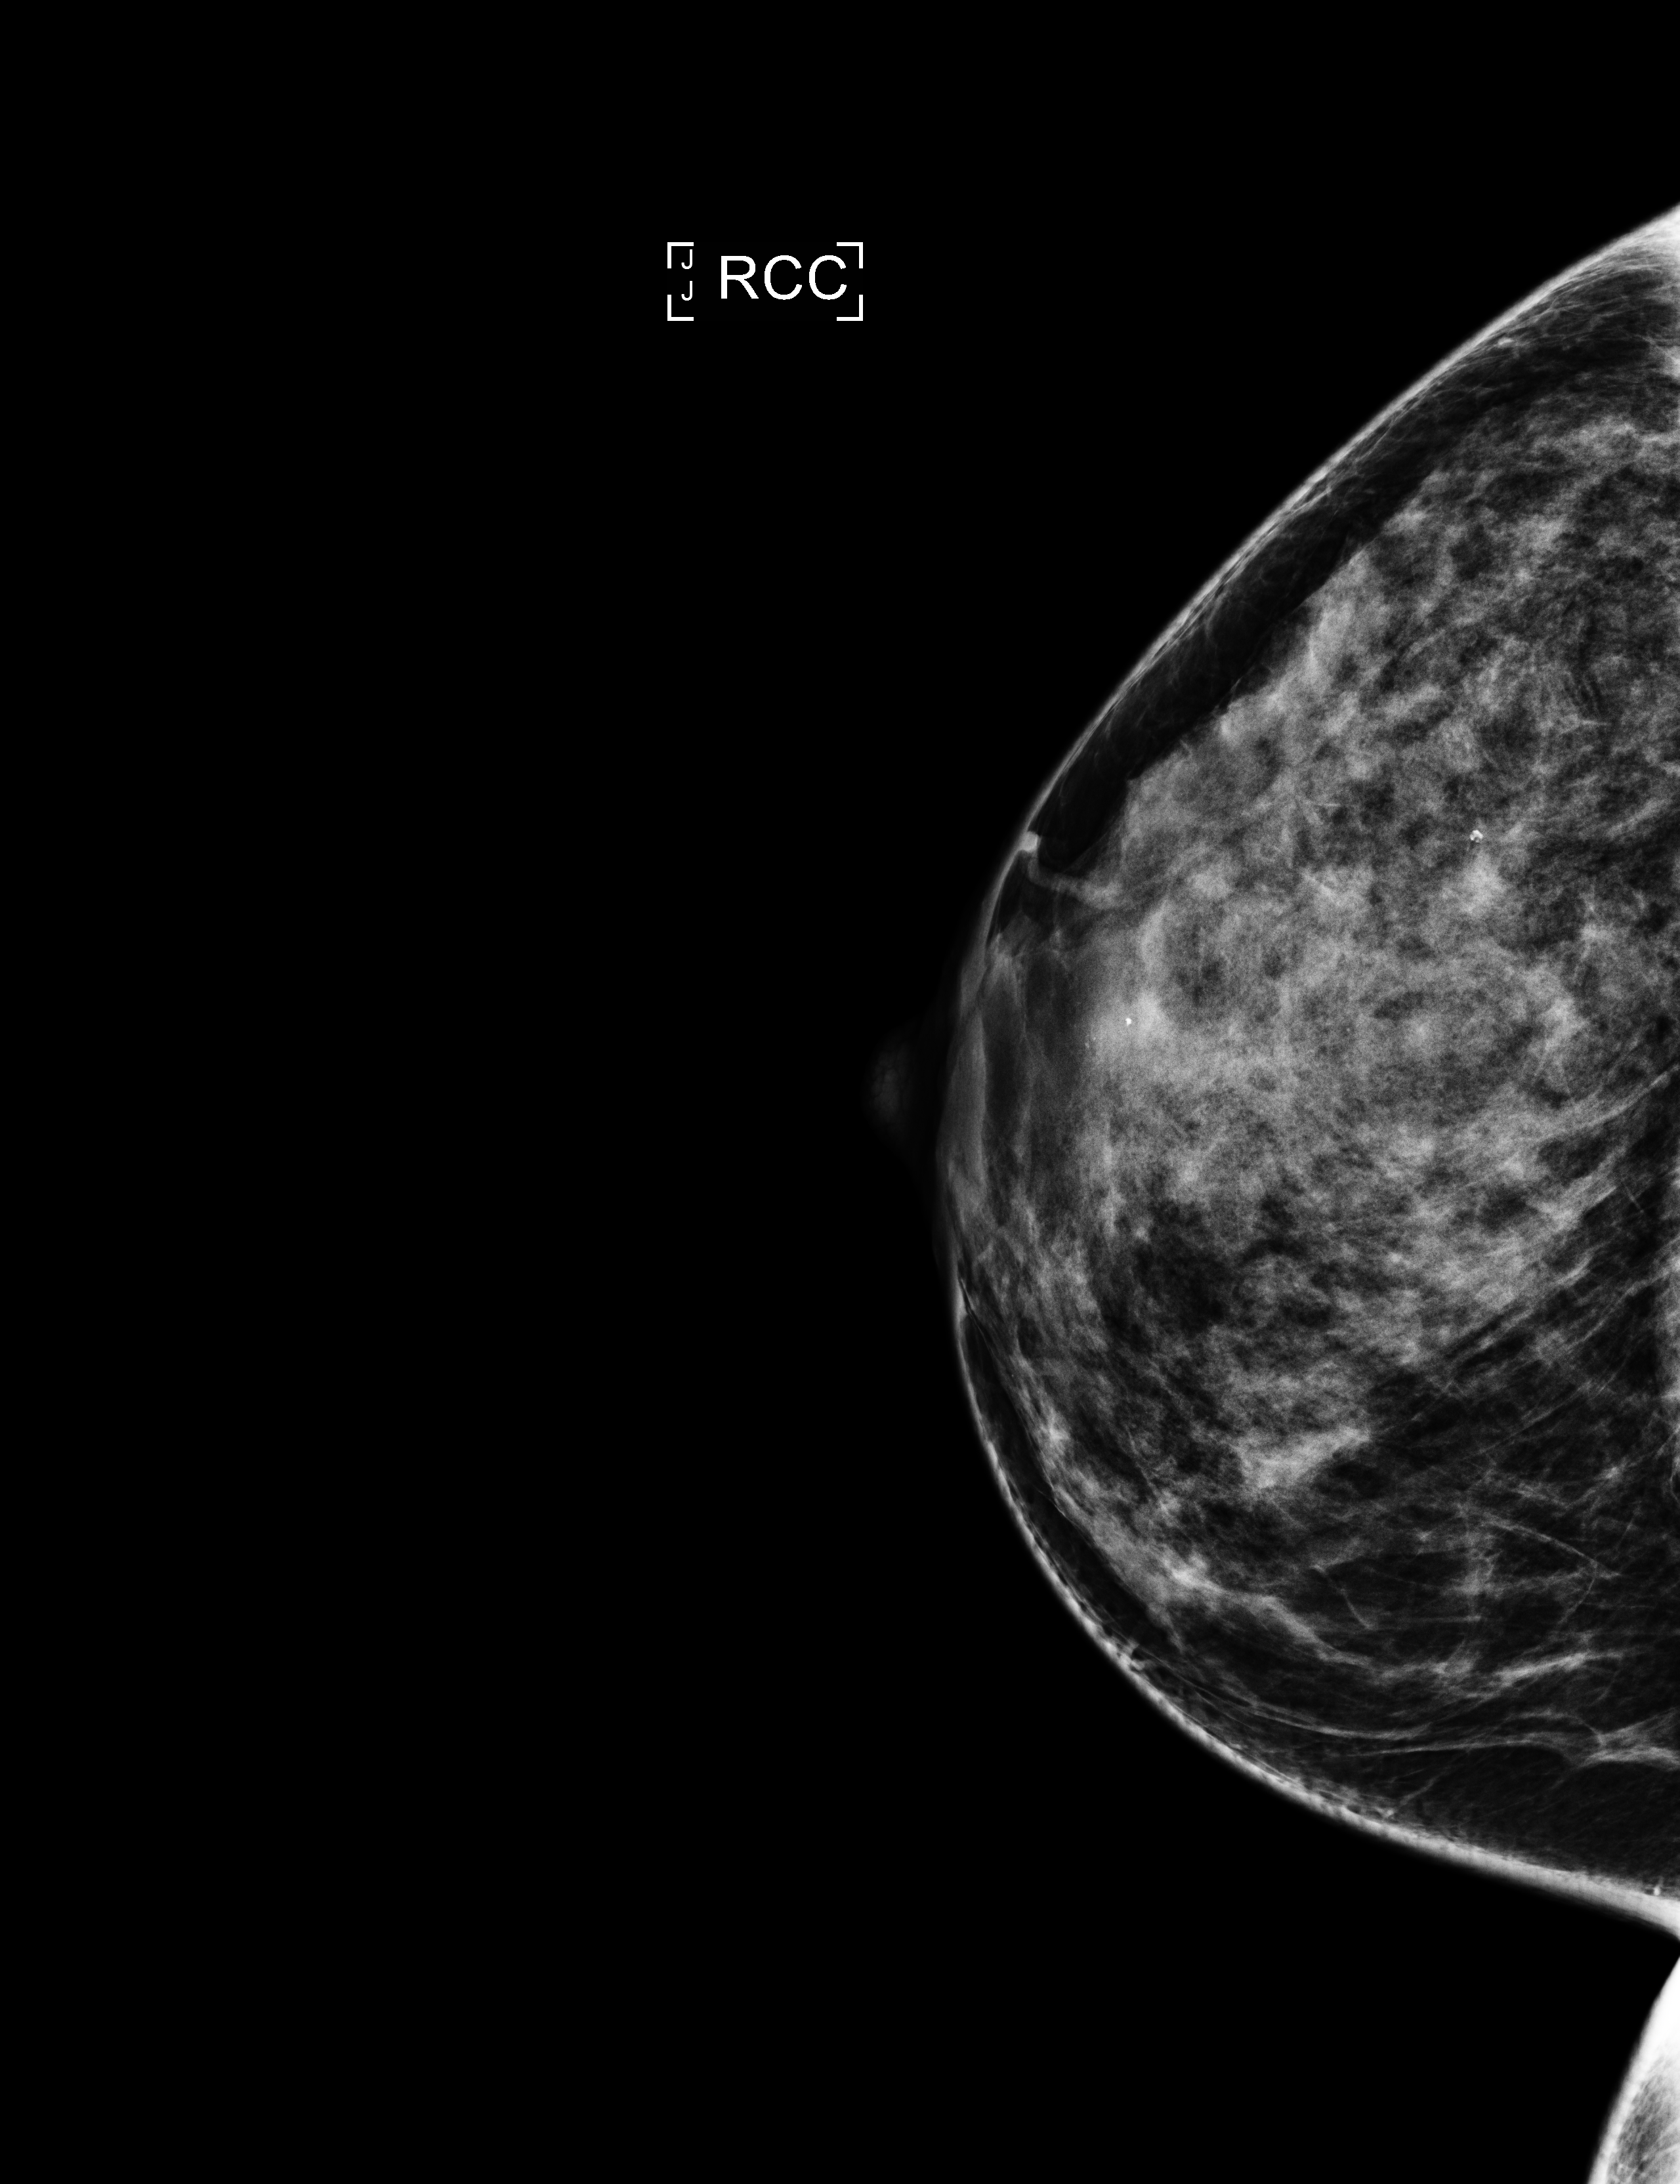
Digital mammogram (FFDM); right breast; CC view; annual screening mammography examination; system: Selenia Dimensions. Patient: female, 43 years.
Final BI-RADS category for the screening round (tomosynthesis exam, both breasts): category 1.